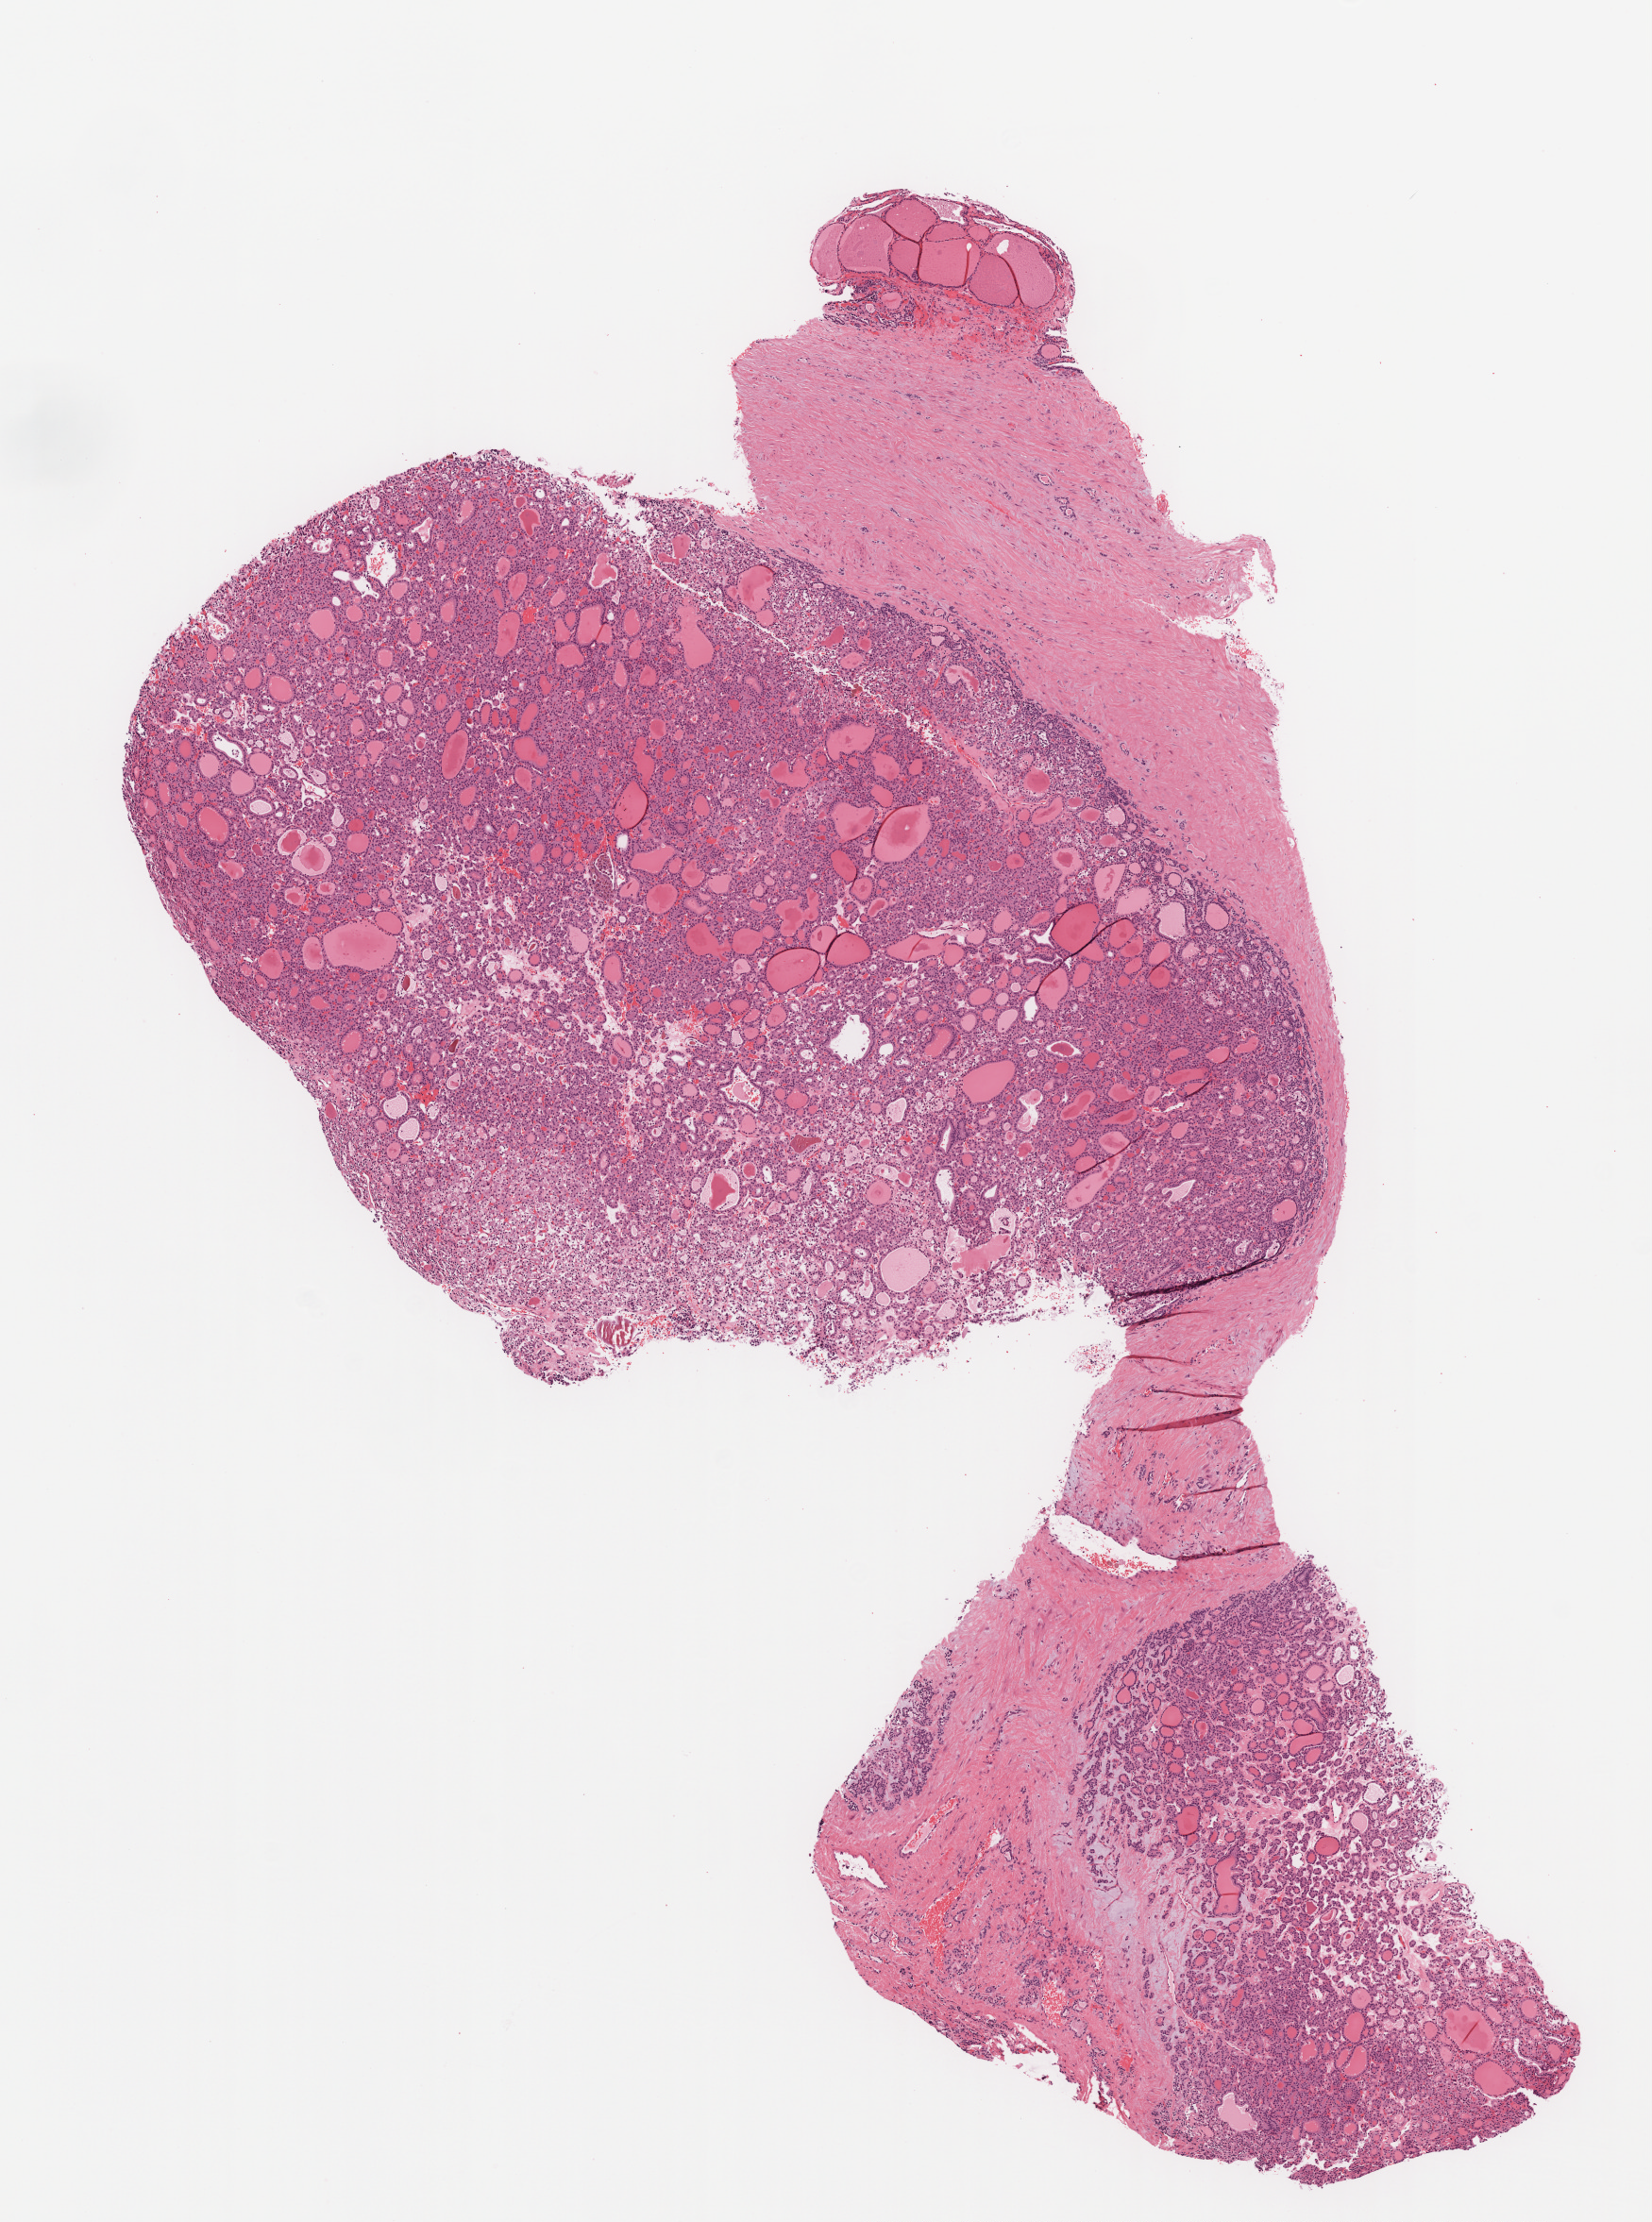
Digitized Hematoxylin and eosin (H&E) stained tissue section (whole slide), a low-resolution overview of the entire scanned area, about 7.0 x 9.4 mm (from a 20x scan). Formalin-fixed paraffin-embedded (FFPE) diagnostic section. Primary tumour sample from the thyroid. Female patient; age at initial diagnosis 33 years.
• laterality: right
• histologic diagnosis: Papillary carcinoma, follicular variant (thyroid gland)
• AJCC pathologic stage: I